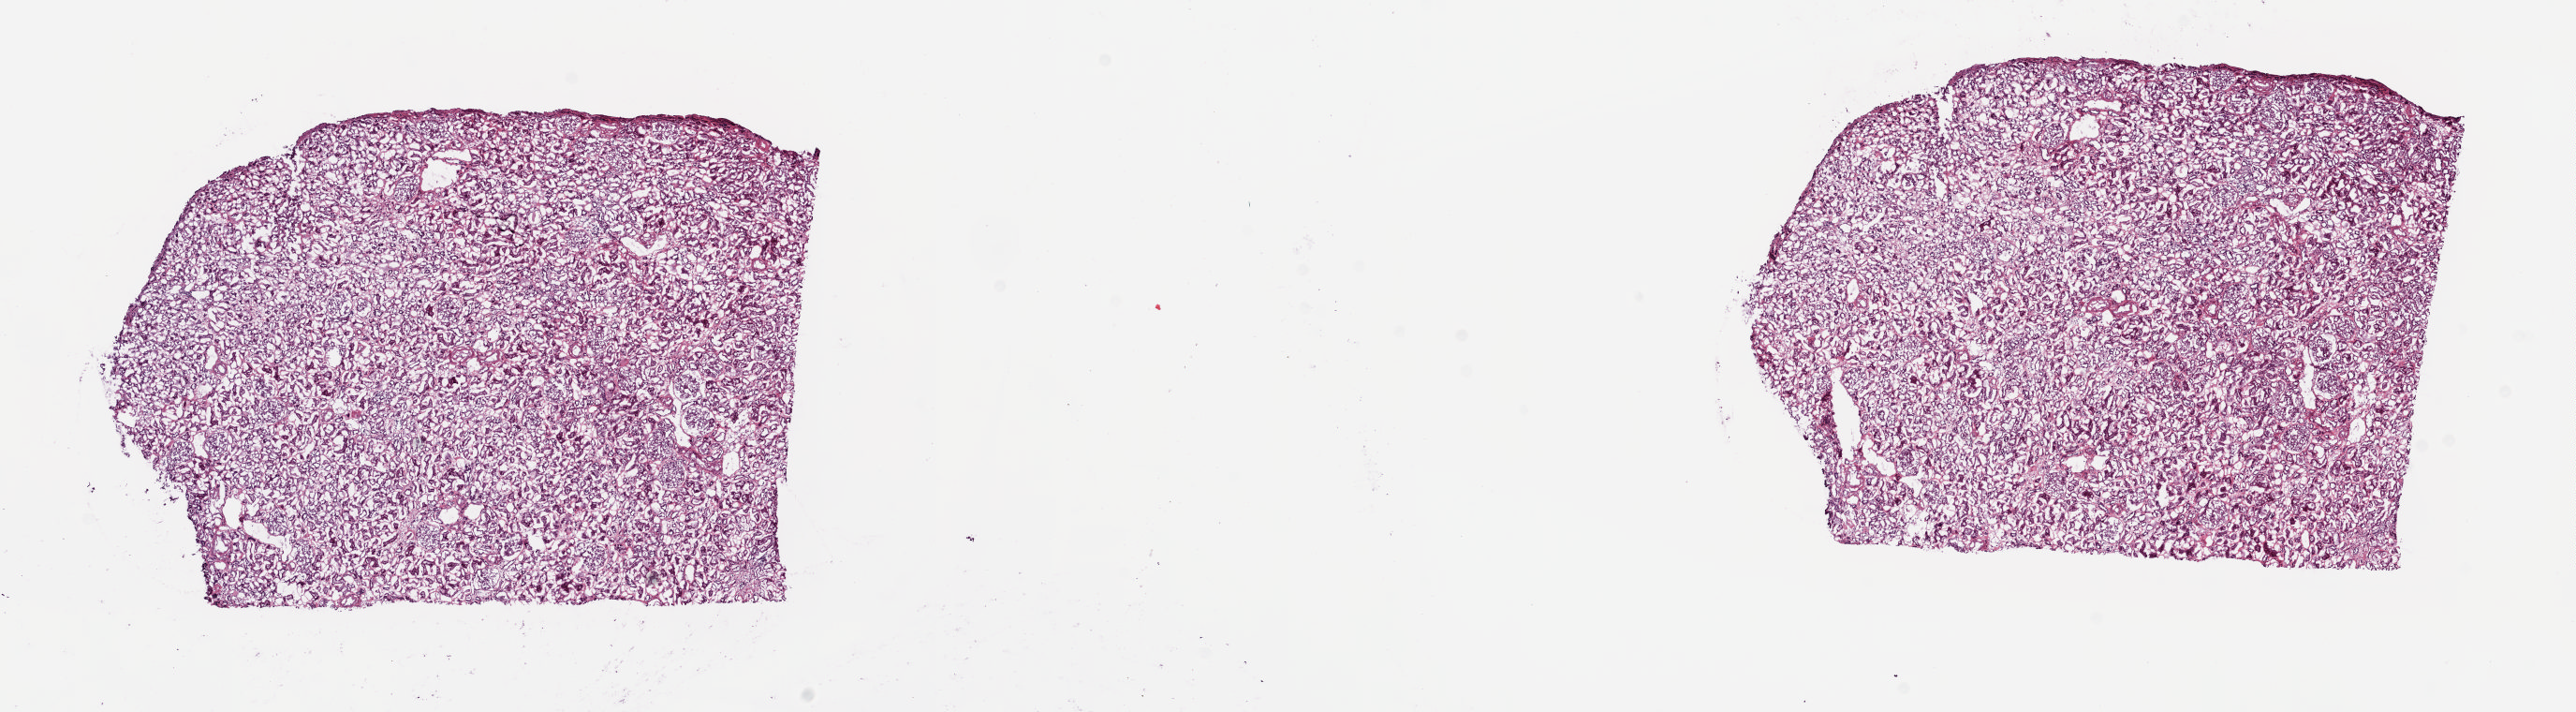
H&E-stained whole-slide image — low-resolution overview of the scanned area, about 21.8 x 6.0 mm (slide scanned at 20x), frozen section, solid tissue normal (non-tumour tissue) sample from the kidney. Male, age 63 years at initial diagnosis. Pathologist review of this section (percent, as recorded): tumour cells 0%, tumour nuclei 0%, normal cells 65%, stromal cells 35%, necrosis 0%. Inflammatory infiltration, as recorded: lymphocyte infiltration 3%, monocyte infiltration 2%, neutrophil infiltration 0%.
- this section: solid tissue normal (non-tumour) sample from the same patient
- patient diagnosis: Papillary adenocarcinoma, NOS